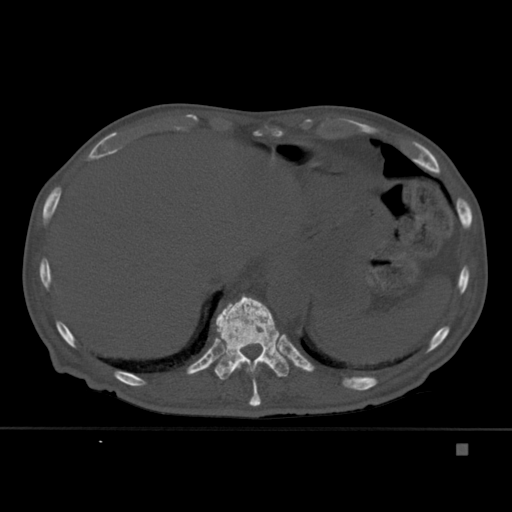
CT including the spine, one axial slice. Position 221 of 451 along the scan axis. Bone window (W 1800 / L 400 HU). 1.5 mm slice thickness. 512 × 512 image matrix, field of view 378 × 378 mm. Patient: male, 75 years. From the clinical record (not read from this slice): primary cancer: prostate.
Structures marked on this image (semi-automatically segmented with operator editing):
- T10 vertebra: box from (x=230, y=364) to (x=261, y=407) px
- T11 vertebra: (x=214, y=294)–(x=289, y=380)